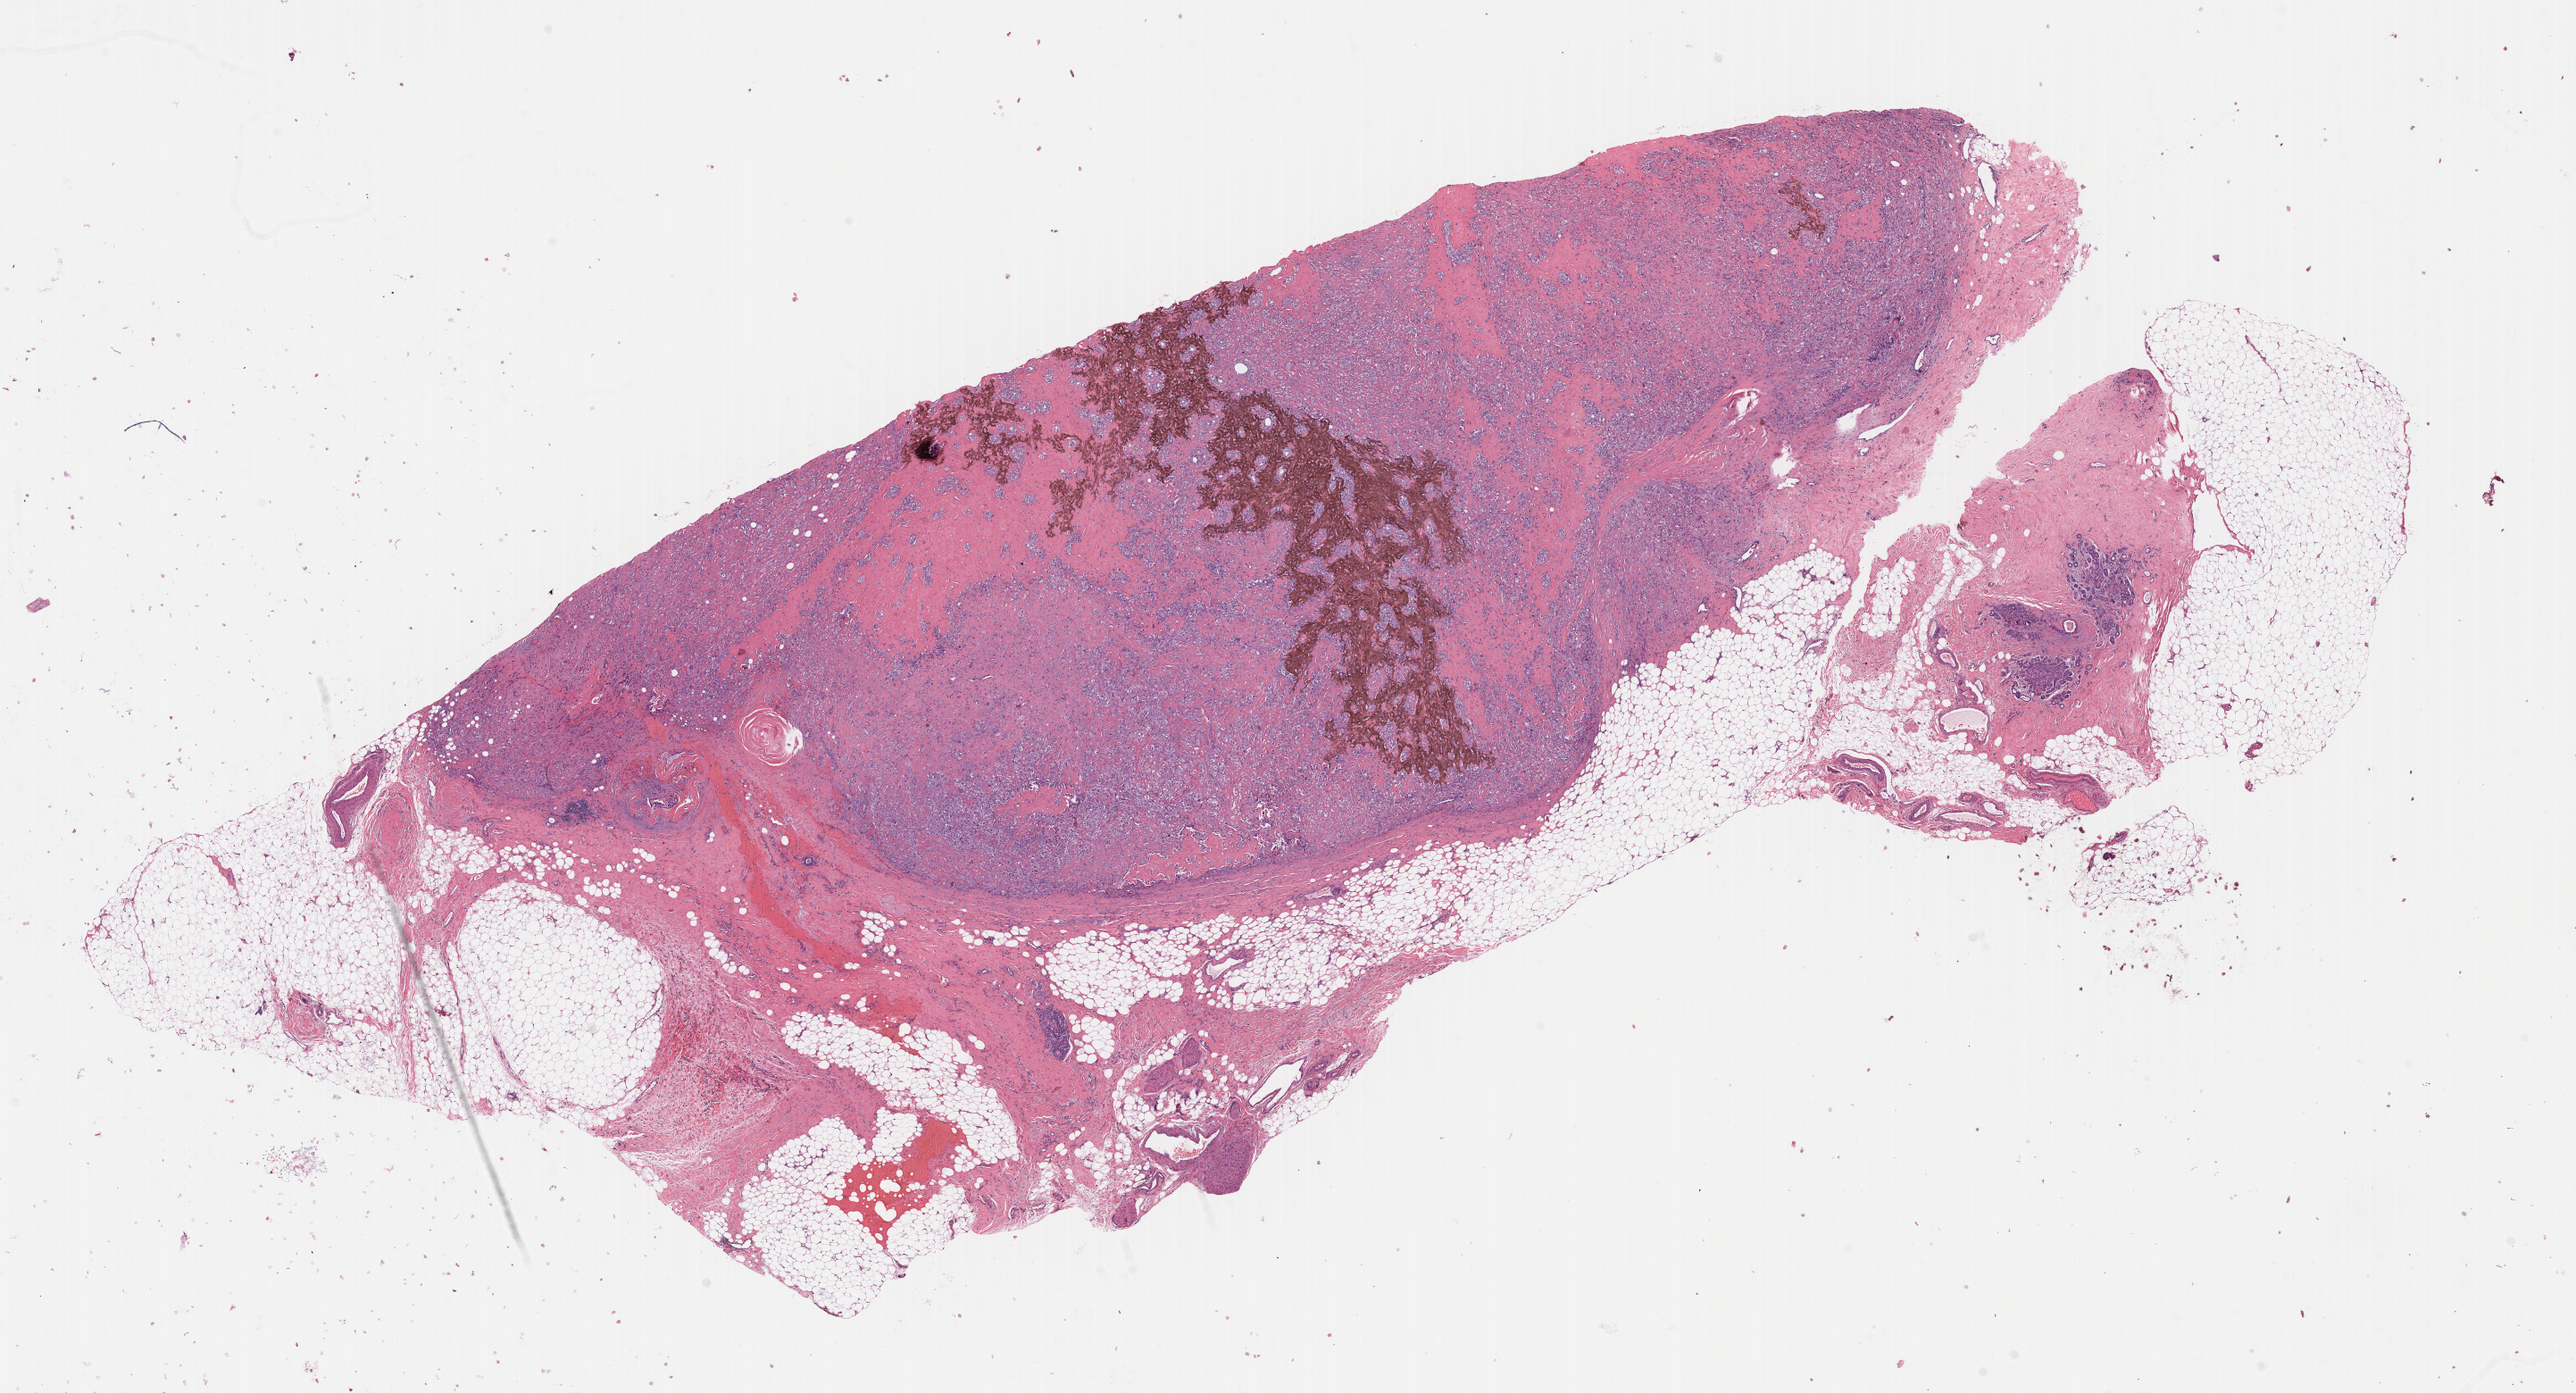
H&E-stained whole-slide image — low-resolution overview of the scanned area, about 22.8 x 12.3 mm (slide scanned at 40x), FFPE section, primary tumour sample from the breast. Female patient; age at initial diagnosis 66 years.
• laterality: right
• diagnosis: Metaplastic carcinoma, NOS
• AJCC pathologic stage: IIA